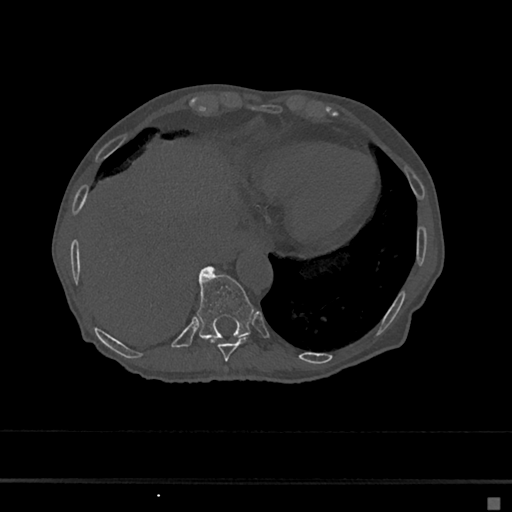
CT including the spine, one axial slice. Slice 244 of 797 in the series (ordered by position). Bone window (W 1800 / L 400 HU). 512 × 512 image matrix. Female patient, age 68 years. Case-level facts recorded for this patient, not image findings: primary cancer: renal.
Annotated regions visible in this slice (semi-automatically segmented with operator editing):
- T10 vertebra: box from (x=197, y=267) to (x=254, y=339) px
- T9 vertebra: (x=210, y=336)–(x=248, y=362)